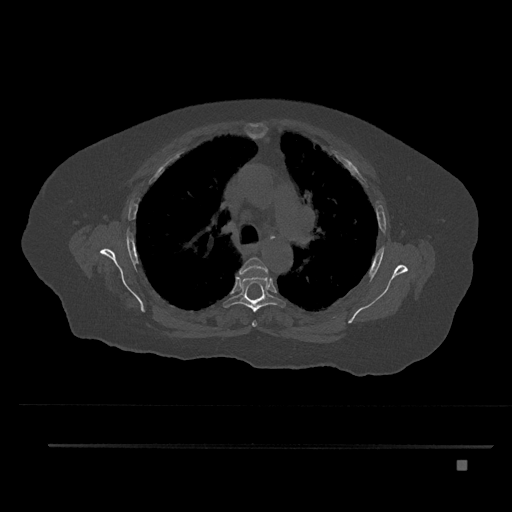
CT including the spine, one axial slice; position 575 of 797 along the scan axis; reconstruction kernel Br40s/3; bone window (W 1800 / L 400 HU); 512 × 512 image matrix, field of view 437 × 437 mm. Female patient, age 76 years. Case-level facts recorded for this patient, not image findings: primary cancer: lung.
Structures marked on this image (semi-automatically segmented with operator editing):
- T4 vertebra: bounding box (x1, y1, x2, y2) in pixels: (239, 257, 268, 327)
- T5 vertebra: (223, 277, 286, 312)